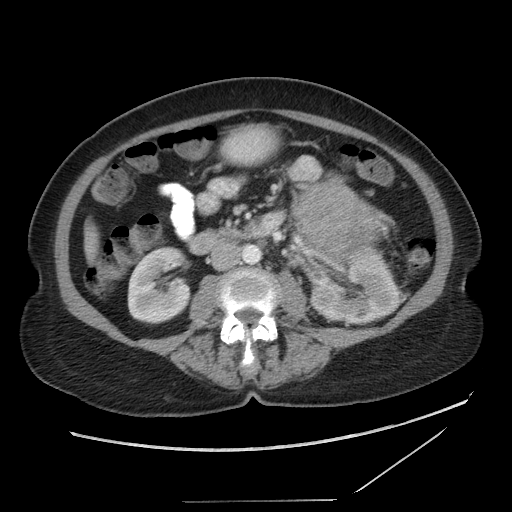
Contrast-enhanced abdominal CT, one axial slice; intravenous contrast given; soft-tissue window (W 400 / L 40 HU); 512 × 512 image matrix. Female patient, age 77 years. Case-level facts recorded for this patient, not image findings: diagnosis: adrenocortical carcinoma; tumour side: left adrenal; tumour size at pathology: 13.1 cm; Ki-67 index: 10 %; stage (as recorded): 3.
Structures marked on this image (semi-automatically segmented with operator editing):
- mass: box from (x=294, y=180) to (x=387, y=261) px